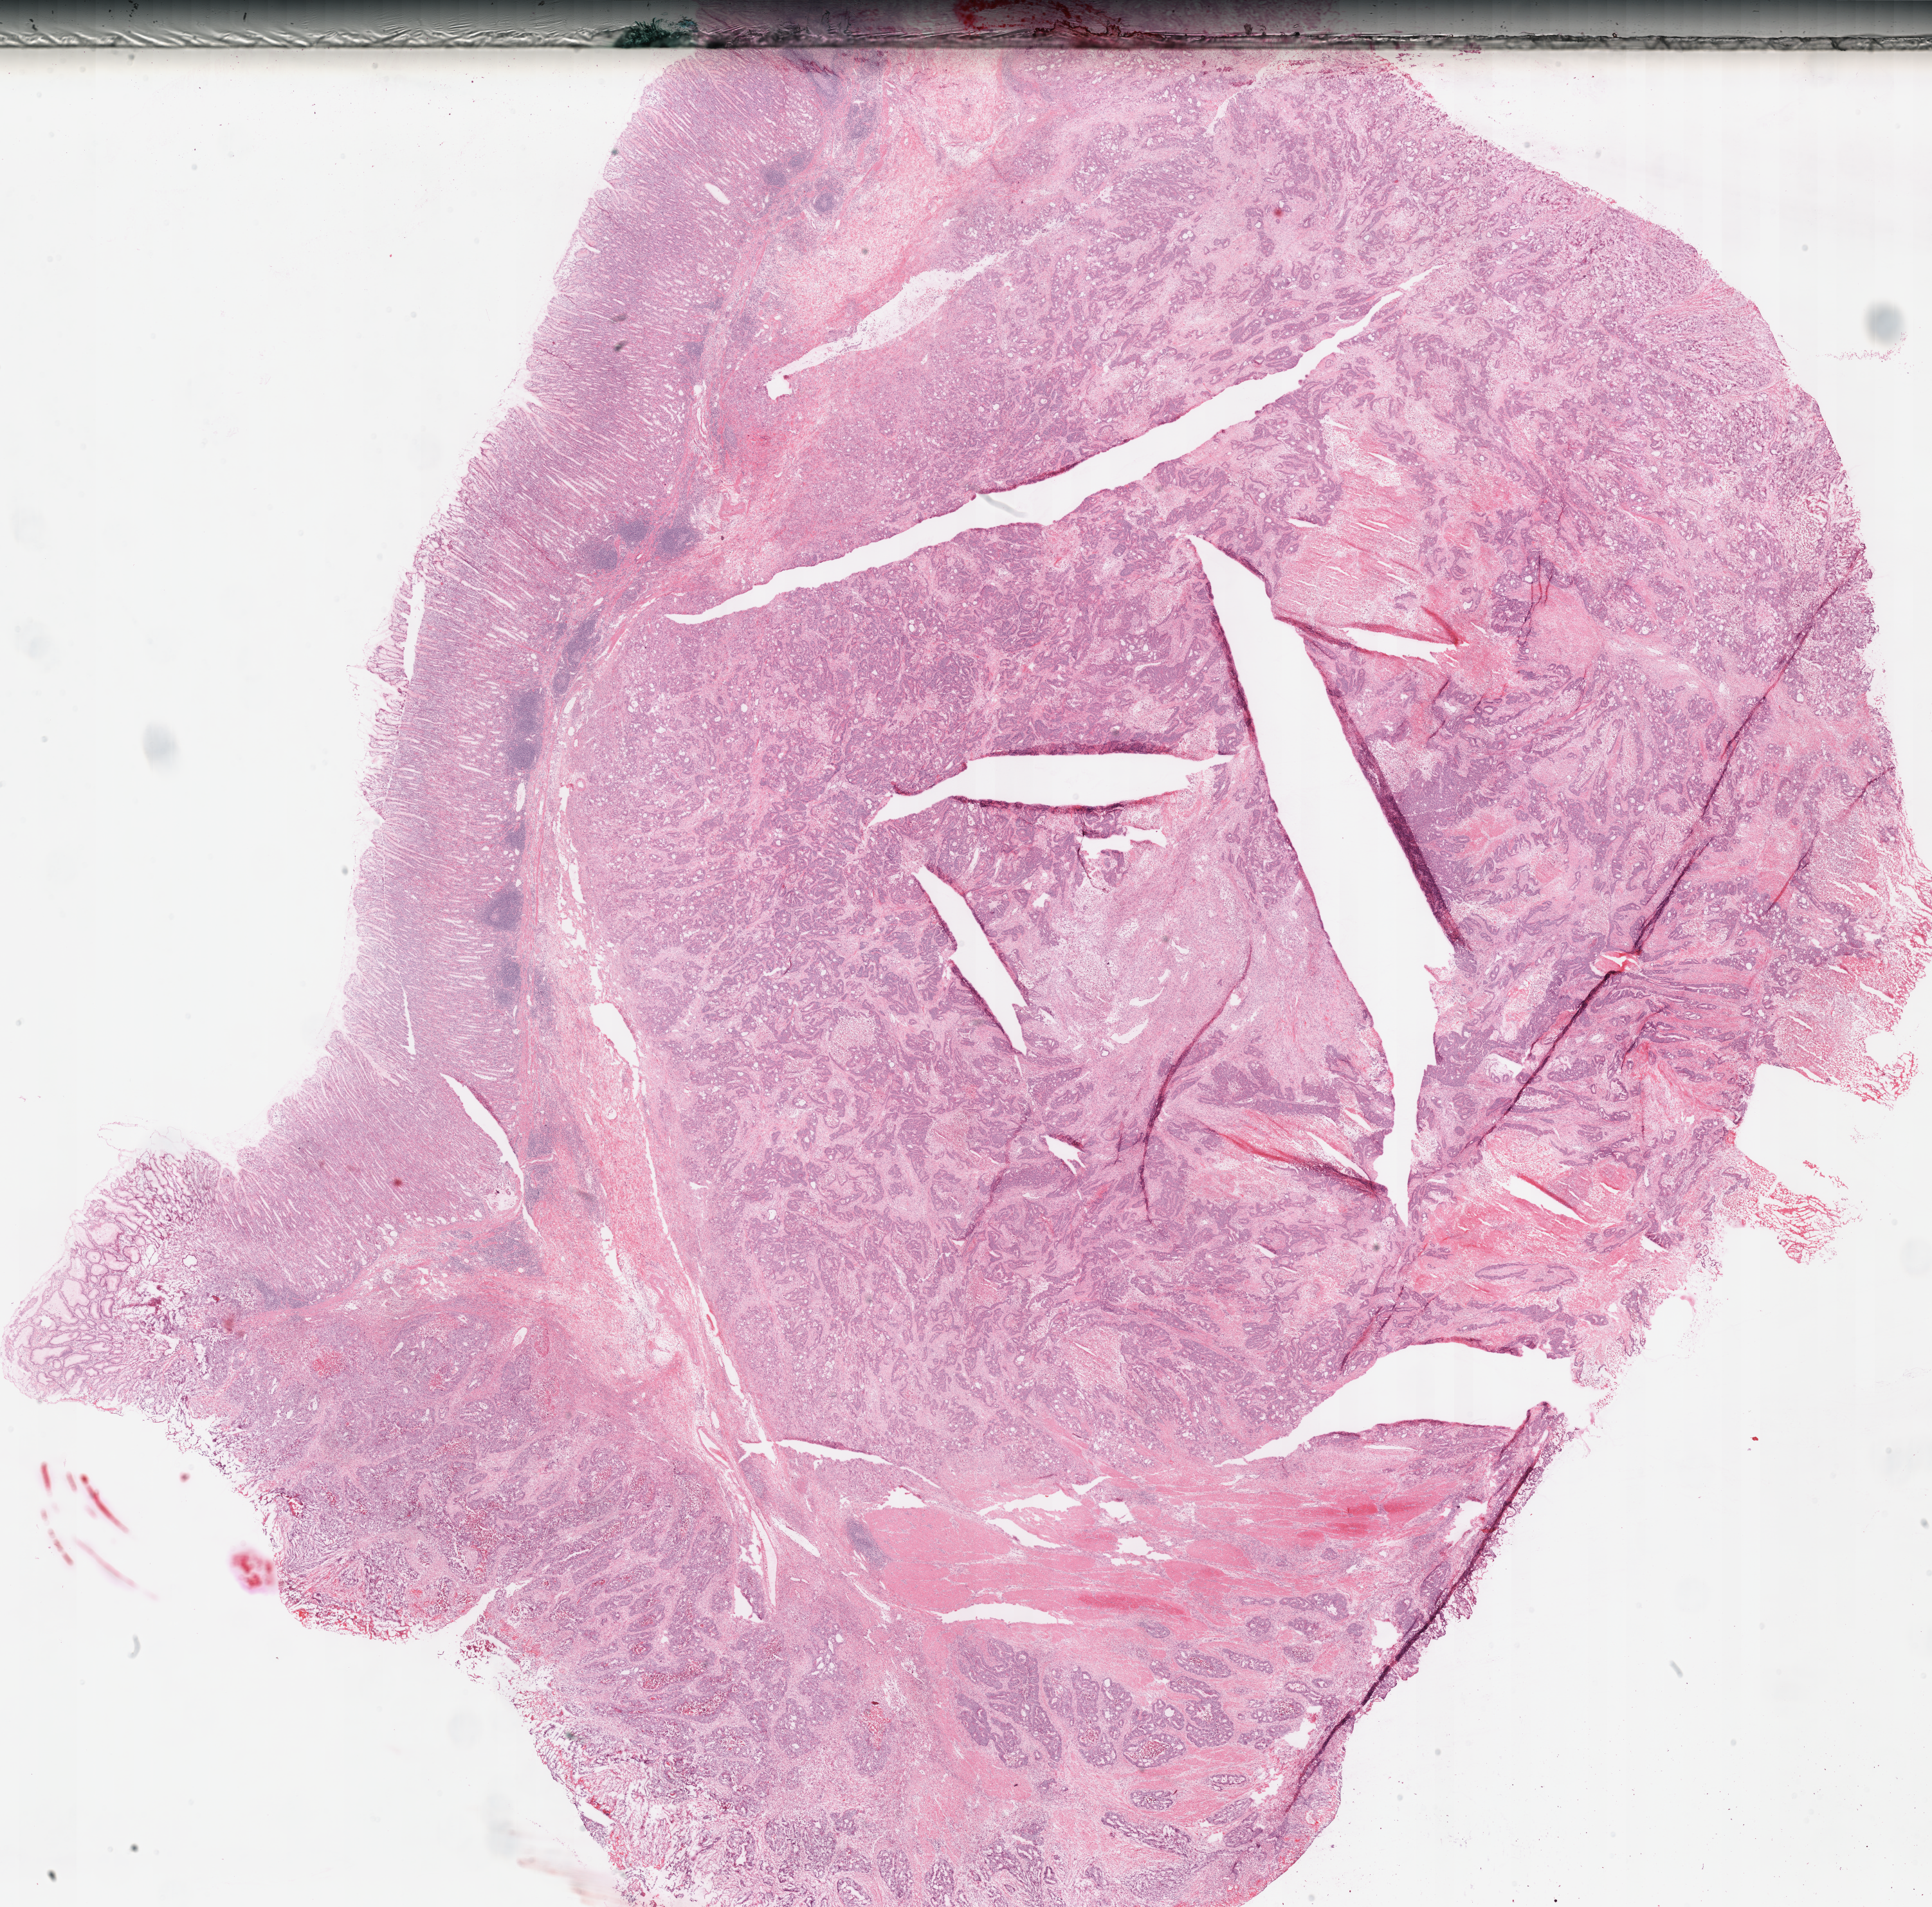
Hematoxylin and eosin (H&E) stained whole-slide image — shown as a low-resolution overview of the whole scanned area (about 23.7 x 23.4 mm, slide scanned at 40x), frozen section, sample: primary tumour, stomach. Male patient; age at initial diagnosis 45 years. Composition of this section per pathologist review: tumour cells 78%, tumour nuclei 75%.
Histologic diagnosis: Tubular adenocarcinoma (gastric antrum).